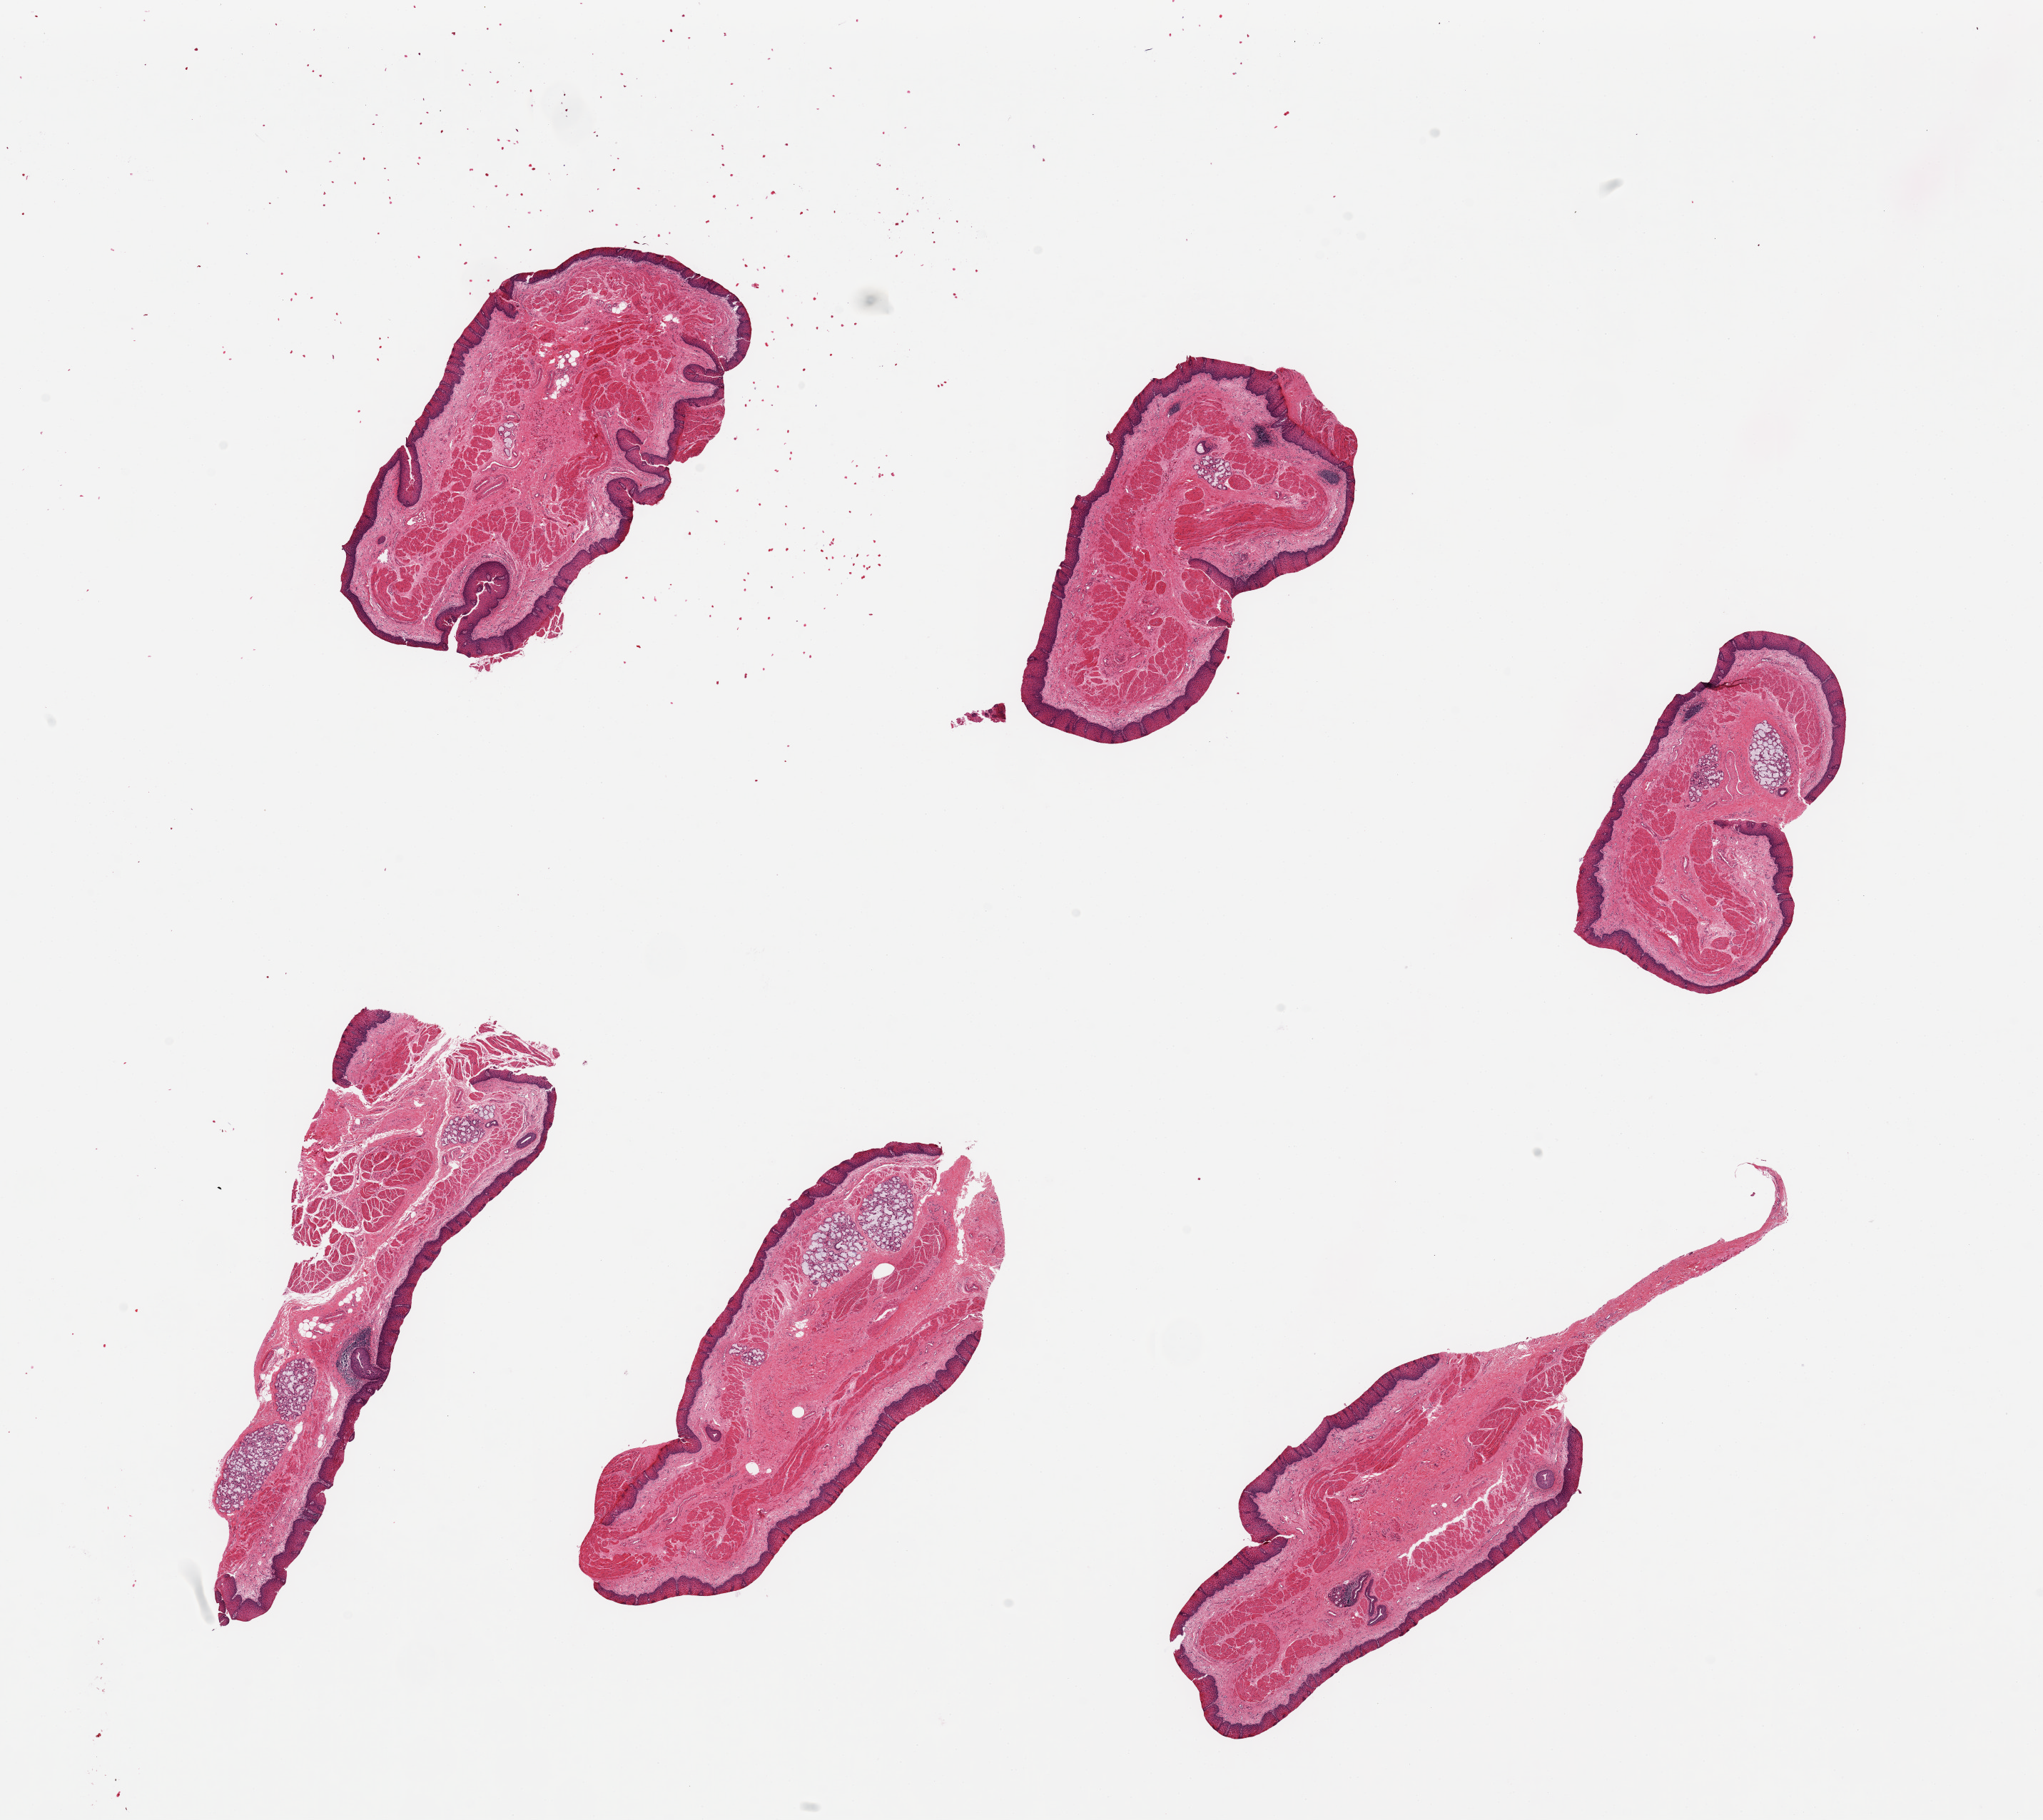
Digitized haematoxylin and eosin-stained section — a low-resolution overview of the entire scanned area, about 22.6 x 20.2 mm, PAXgene-fixed paraffin-embedded (PFPE) section, sampled site (target tissue): esophageal mucous membrane, donor tissue sample. Donor: male.
- pathologist's review note for this sample: 6 pieces ~6x1.5mm. Squamous mucosa up to ~200 microns thick or ~15%